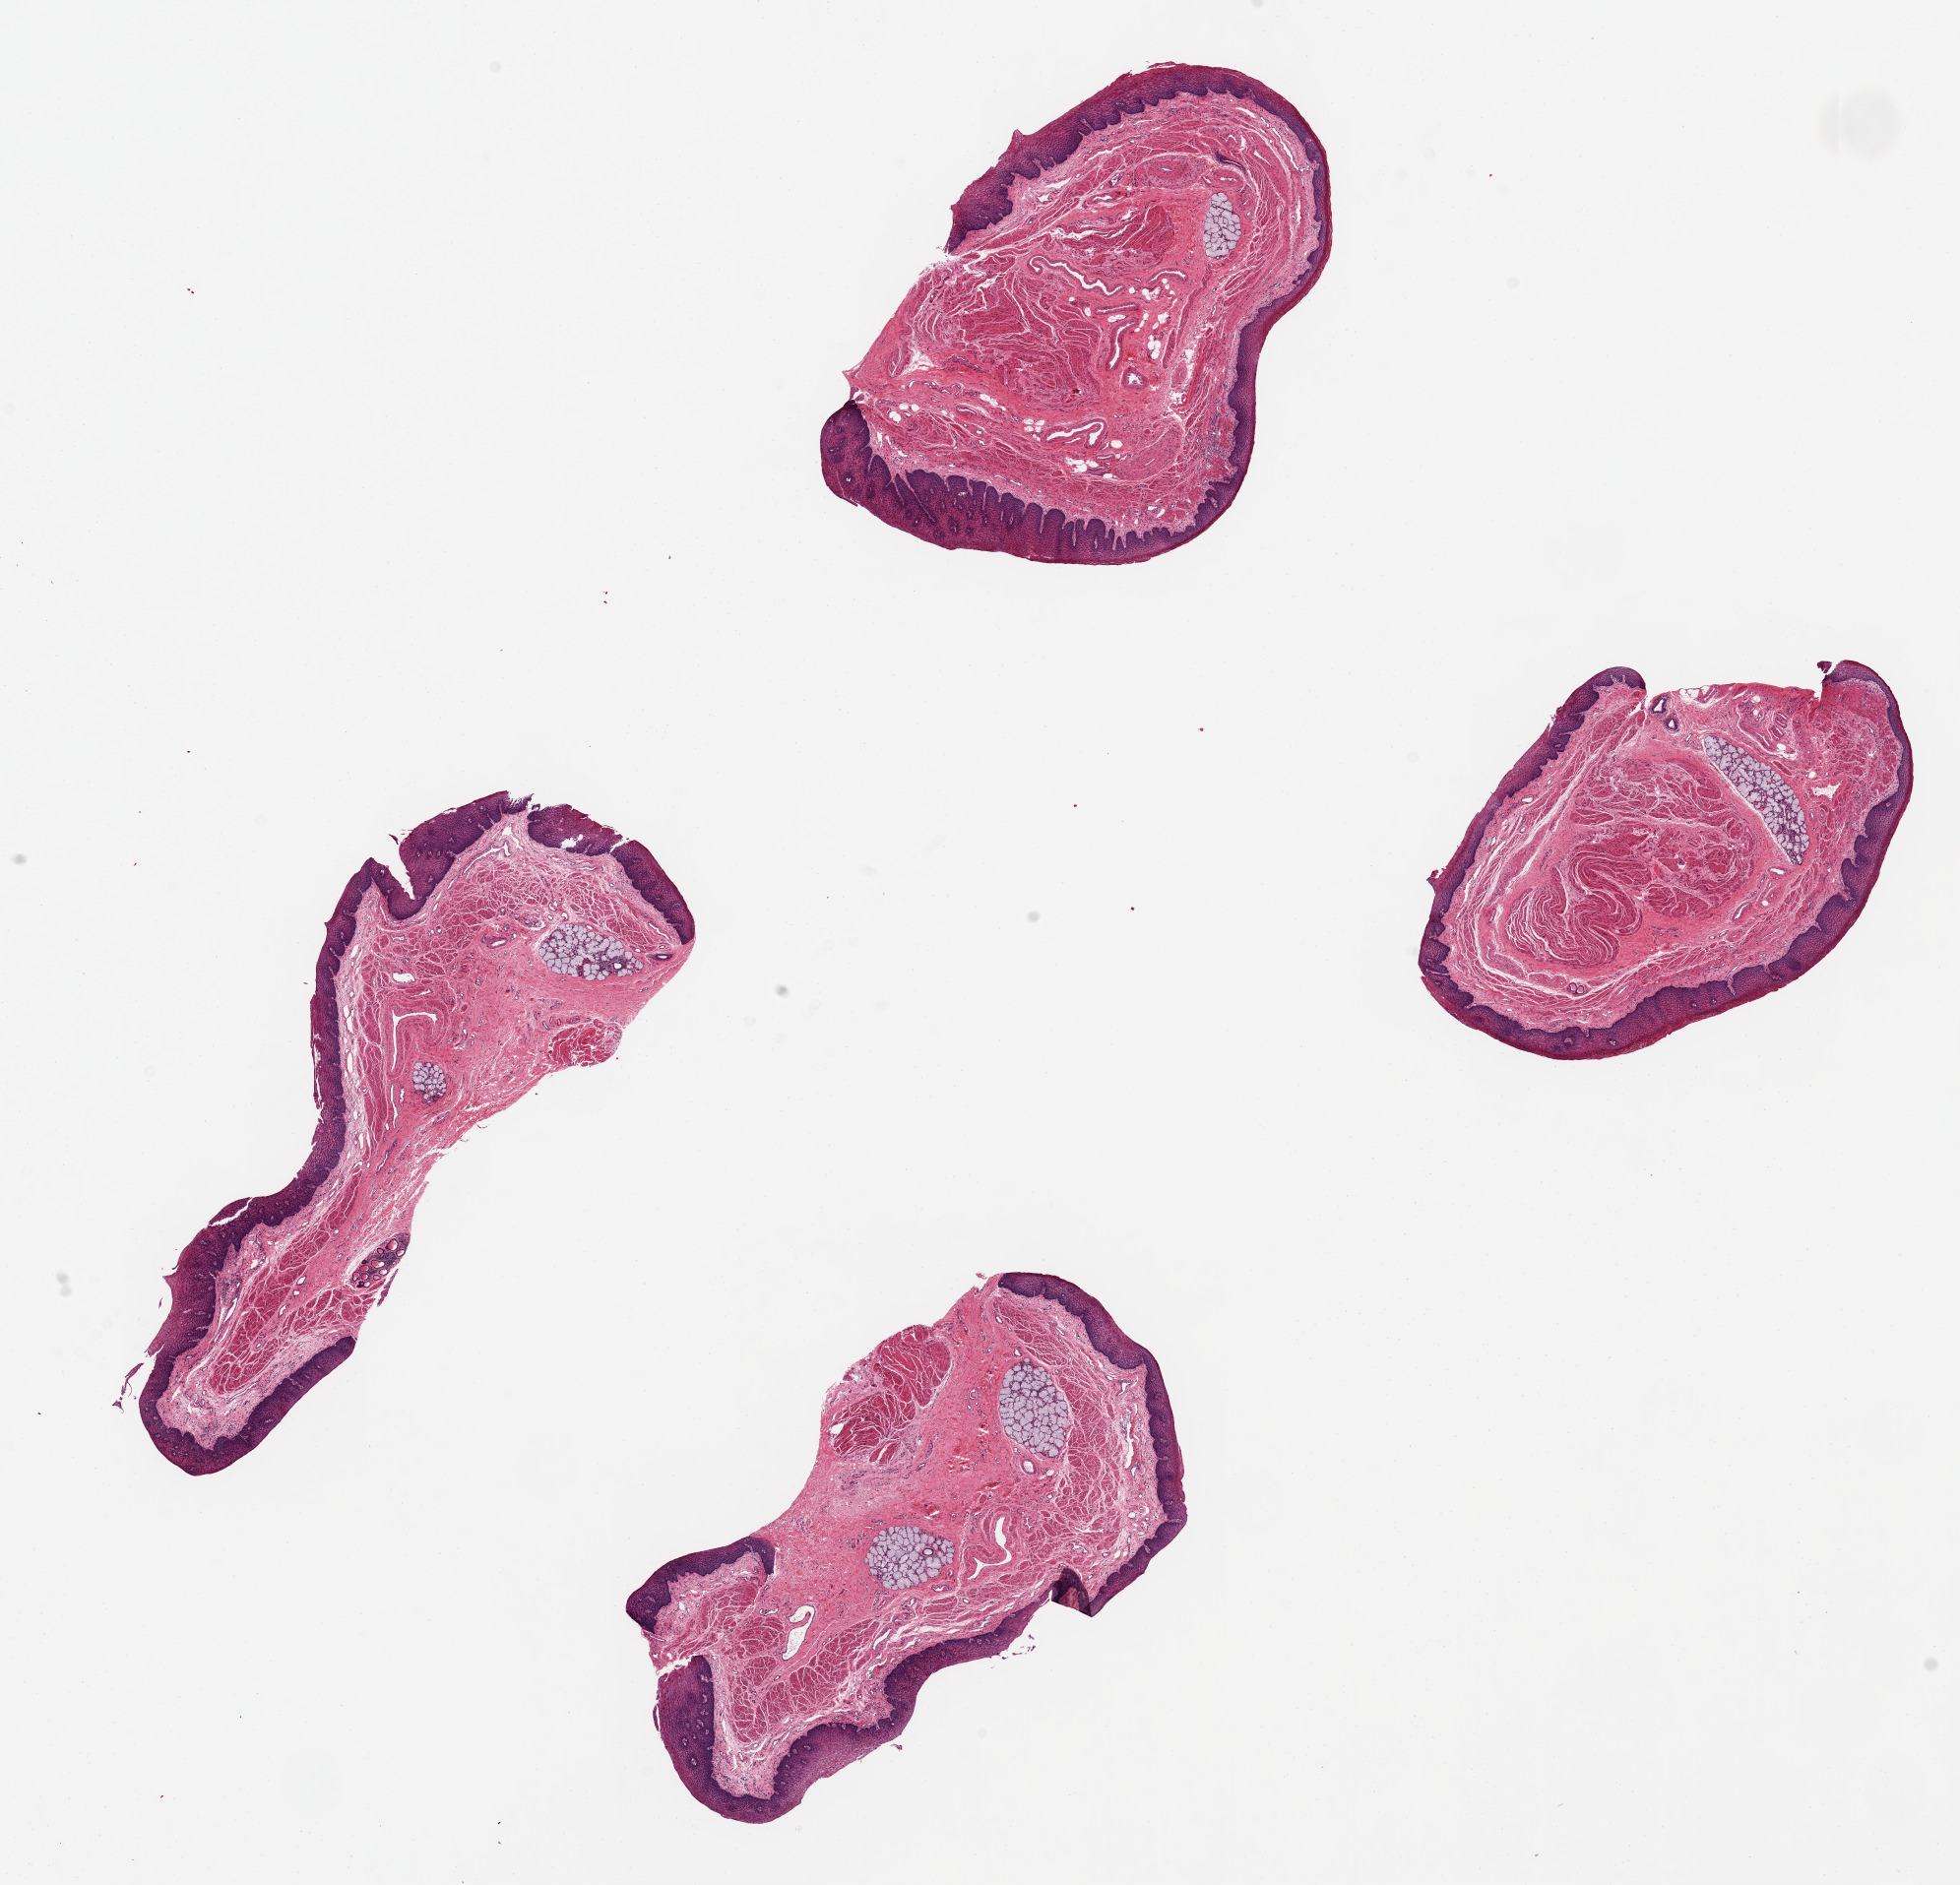
Digitized haematoxylin and eosin-stained section, a low-resolution overview of the entire scanned area, about 15.8 x 15.1 mm (from a 20x scan); PAXgene-fixed, paraffin-embedded tissue; sampled site (target tissue): esophageal mucous membrane; tissue donor sample. Donor sex: male.
- reviewer comment on this tissue sample: 4 5x3mm pieces; squamous mucosa is ~10% of thickness